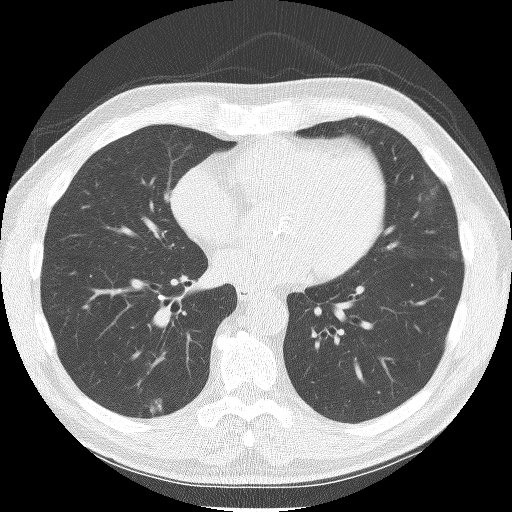
Low-dose screening chest CT, one axial slice. Position 66 of 150 along the scan axis. Reconstruction kernel BONE. Lung window (W 1500 / L -600 HU). 512 × 512 image matrix.
Annotated regions visible in this slice (expert manual segmentation):
- lesion 1 (tumor, lower lobe of right lung): bounding box <150,398,162,413> (left, top, right, bottom; pixels)